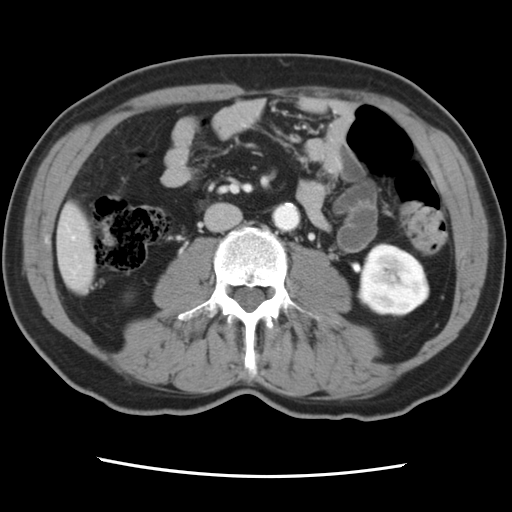
Contrast-enhanced abdominal CT, one axial slice; position 17 of 83 along the scan axis; 120 kVp; soft-tissue window (W 400 / L 40 HU); 5 mm slice thickness; 512 × 512 image matrix, field of view 321 × 321 mm. Male patient, age 69 years. Case-level facts recorded for this patient, not image findings: diagnosis: colorectal cancer liver metastases, imaged before liver resection.
Structures marked on this image (expert manual segmentation):
- hepatic veins: bounding box (x1, y1, x2, y2) in pixels: (72, 236, 74, 238)
- liver: (58, 206, 95, 291)
- planned liver remnant (the part of the liver to remain after resection): (59, 206, 95, 291)